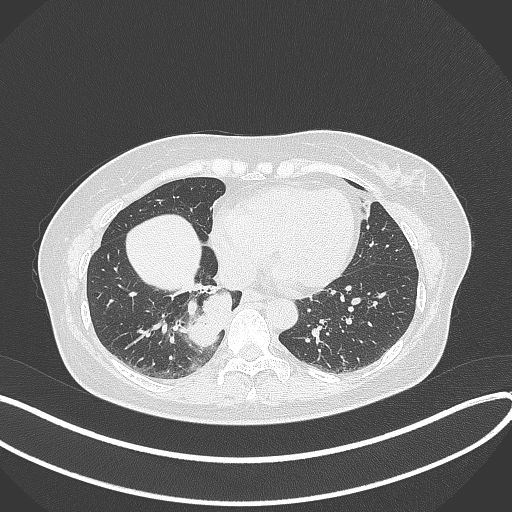
Chest CT, one axial slice; slice 115 of 331 in the series (ordered by position); lung window (W 1500 / L -600 HU); 1 mm slice thickness; 512 × 512 image matrix, field of view 400 × 400 mm. Patient: female, 54 years. From the clinical record (not read from this slice): clinical TNM (as recorded): T4 N0 M0.
Outlined on this slice (rectangle marked by the reading radiologist):
- lung tumour (recorded histology: adenocarcinoma): bounding box [x1, y1, x2, y2] px = [184, 280, 233, 355]